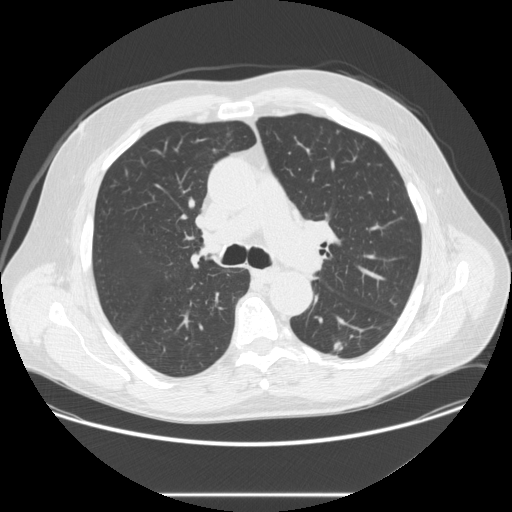
Low-dose screening chest CT, one axial slice. Position 164 of 262 along the scan axis. Lung window (W 1500 / L -600 HU). 2.5 mm slice thickness. 512 × 512 image matrix.
Structures marked on this image (expert manual segmentation):
- lesion 1 (tumor, lower lobe of left lung): bounding box <334,342,343,350> (left, top, right, bottom; pixels)